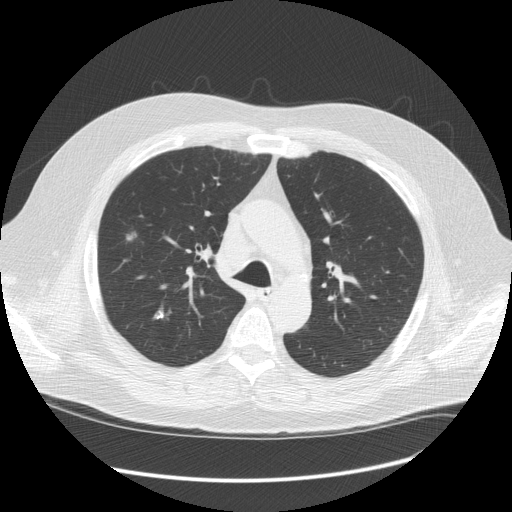
Axial slice from a low-dose chest CT screening exam; third annual screen; lung window (W 1500 / L -600 HU); 2.5 mm slice thickness; slice 39 of 128 in the series; 512 × 512 image matrix, field of view 401 × 401 mm. Male participant, aged 61 years at enrolment.
Expert reader's lesion annotation, bounding box [x1, y1, x2, y2] px = [104, 218, 151, 257]. Reader record for this screening exam (exam-level; its link to the box is not recorded): non-calcified nodule or mass ≥4 mm, right upper lobe, 13 × 11 mm, spiculated (stellate) margins, soft tissue attenuation, pre-existing on the prior screen: yes; interval growth: yes.